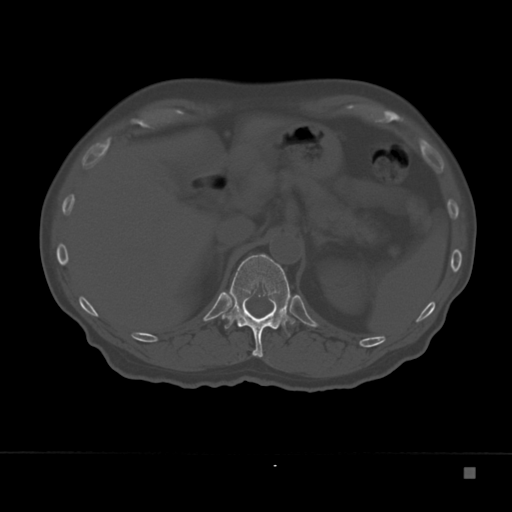
CT including the spine, one axial slice; slice 132 of 332 in the series (ordered by position); reconstruction kernel Br40s; 120 kVp; bone window (W 1800 / L 400 HU); 512 × 512 image matrix, field of view 389 × 389 mm. Male patient, age 72 years. Case-level facts recorded for this patient, not image findings: primary cancer: skeletal.
Outlined on this slice (semi-automatically segmented with operator editing):
- T12 vertebra: bounding box [x1, y1, x2, y2] px = [222, 254, 295, 358]